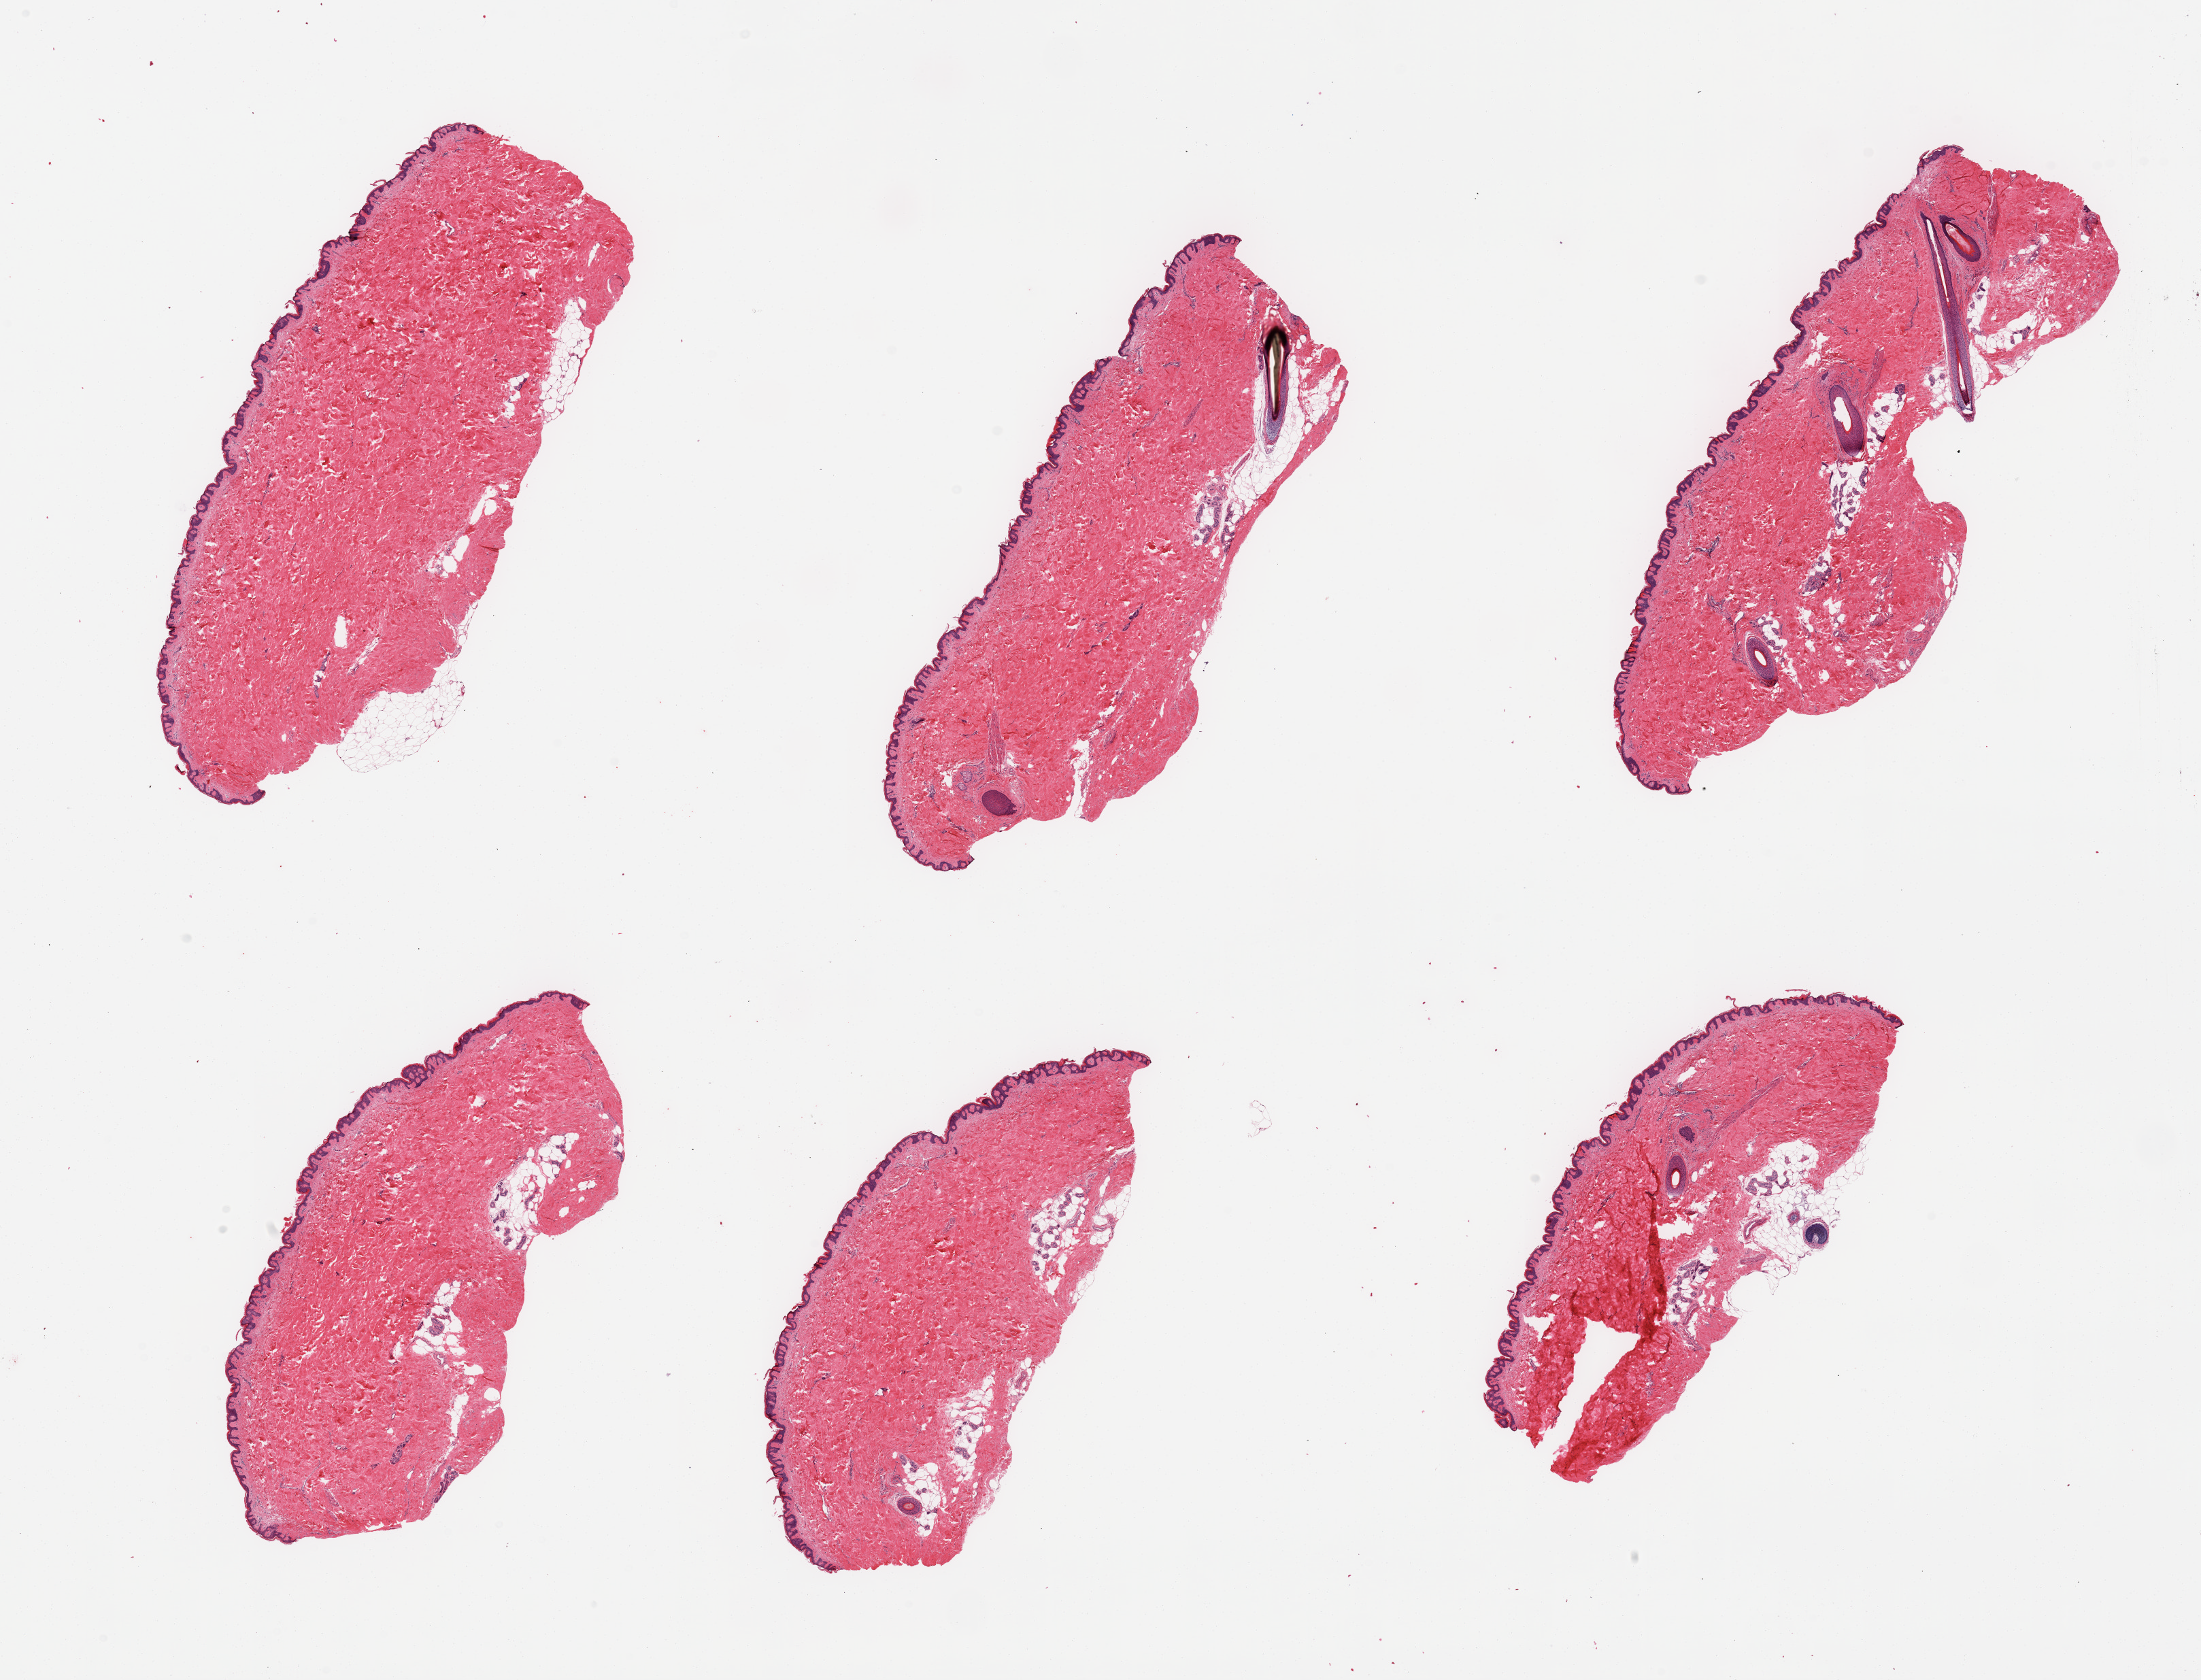
Hematoxylin and eosin (H&E) whole-slide image — shown as a low-resolution overview of the whole scanned area (about 25.6 x 19.5 mm, from a 20x scan); PAXgene-fixed paraffin-embedded (PFPE) section; section of skin of suprapubic region (target tissue); tissue donor sample. Male donor.
Pathologist's review note for this sample: 6 pieces, trace dermal fat; squamous epithelium is ~40 microns.